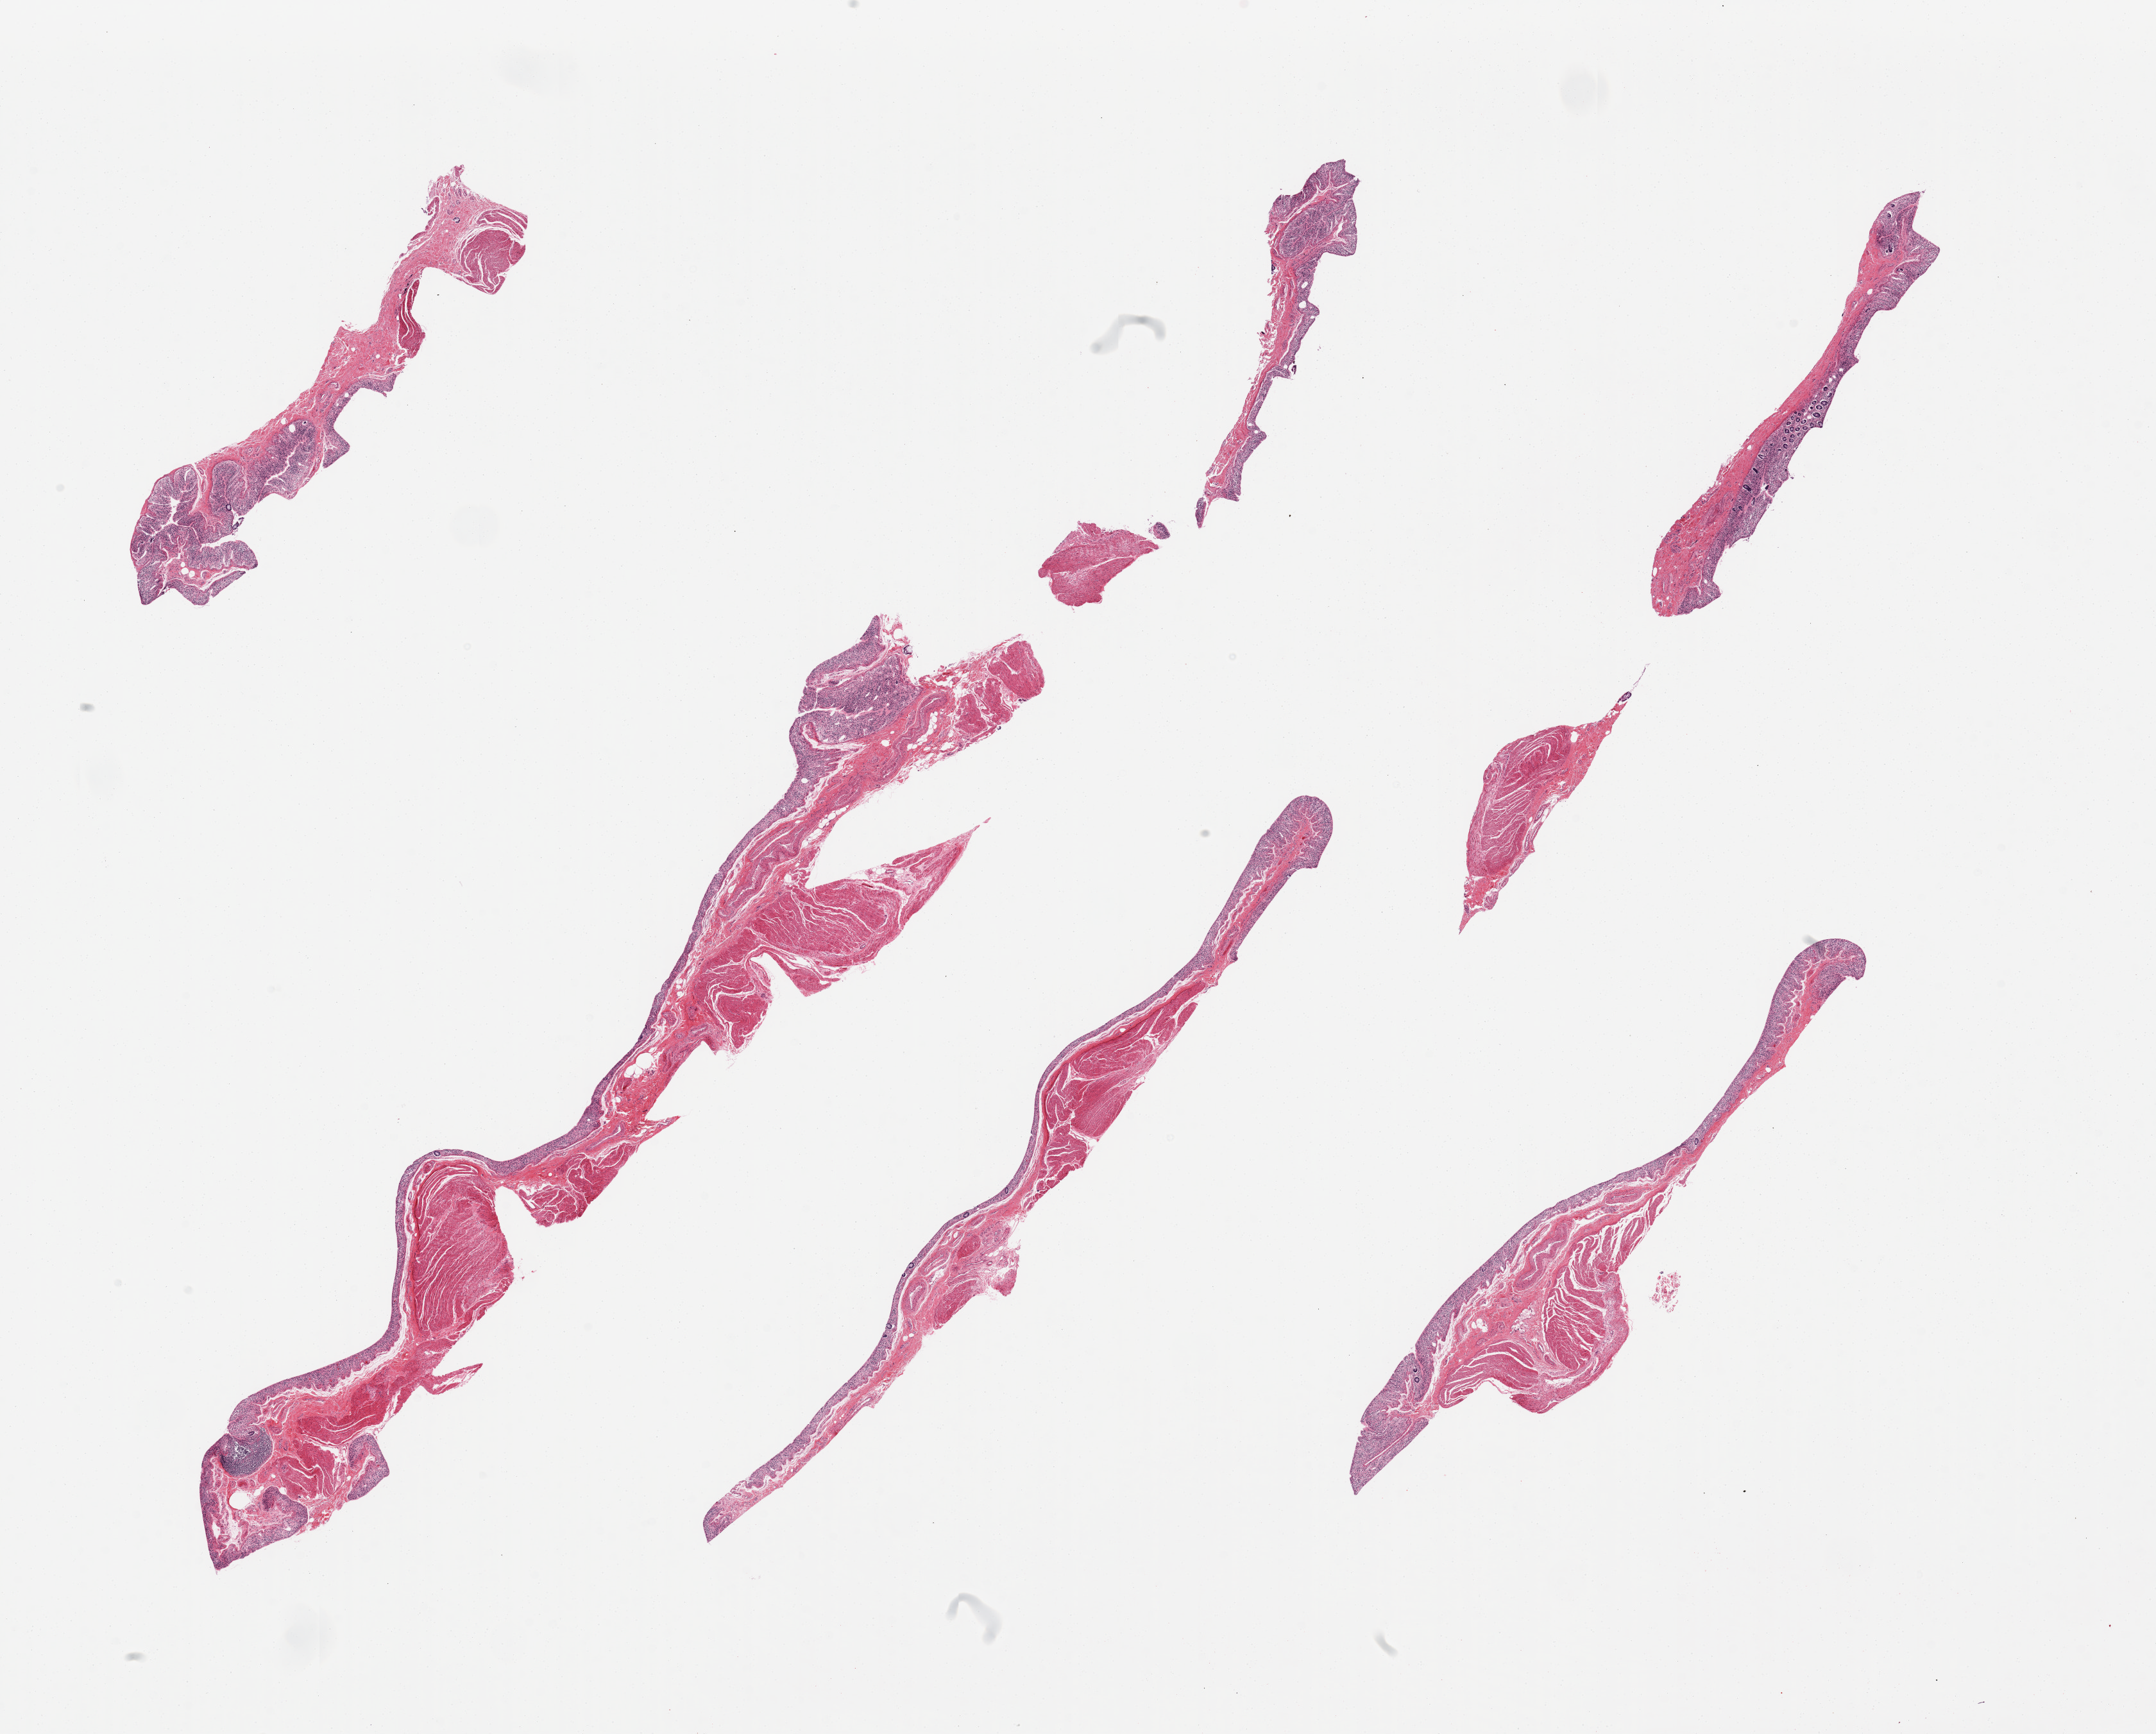
Digitized haematoxylin and eosin-stained section — a low-resolution overview of the entire scanned area, about 26.6 x 21.4 mm, PAXgene-fixed, paraffin-embedded tissue, section of transverse colon (target tissue), donor tissue sample. Donor sex: male.
• review note (as recorded): 8 pieces, muscularis and severely autolyzed mucosa